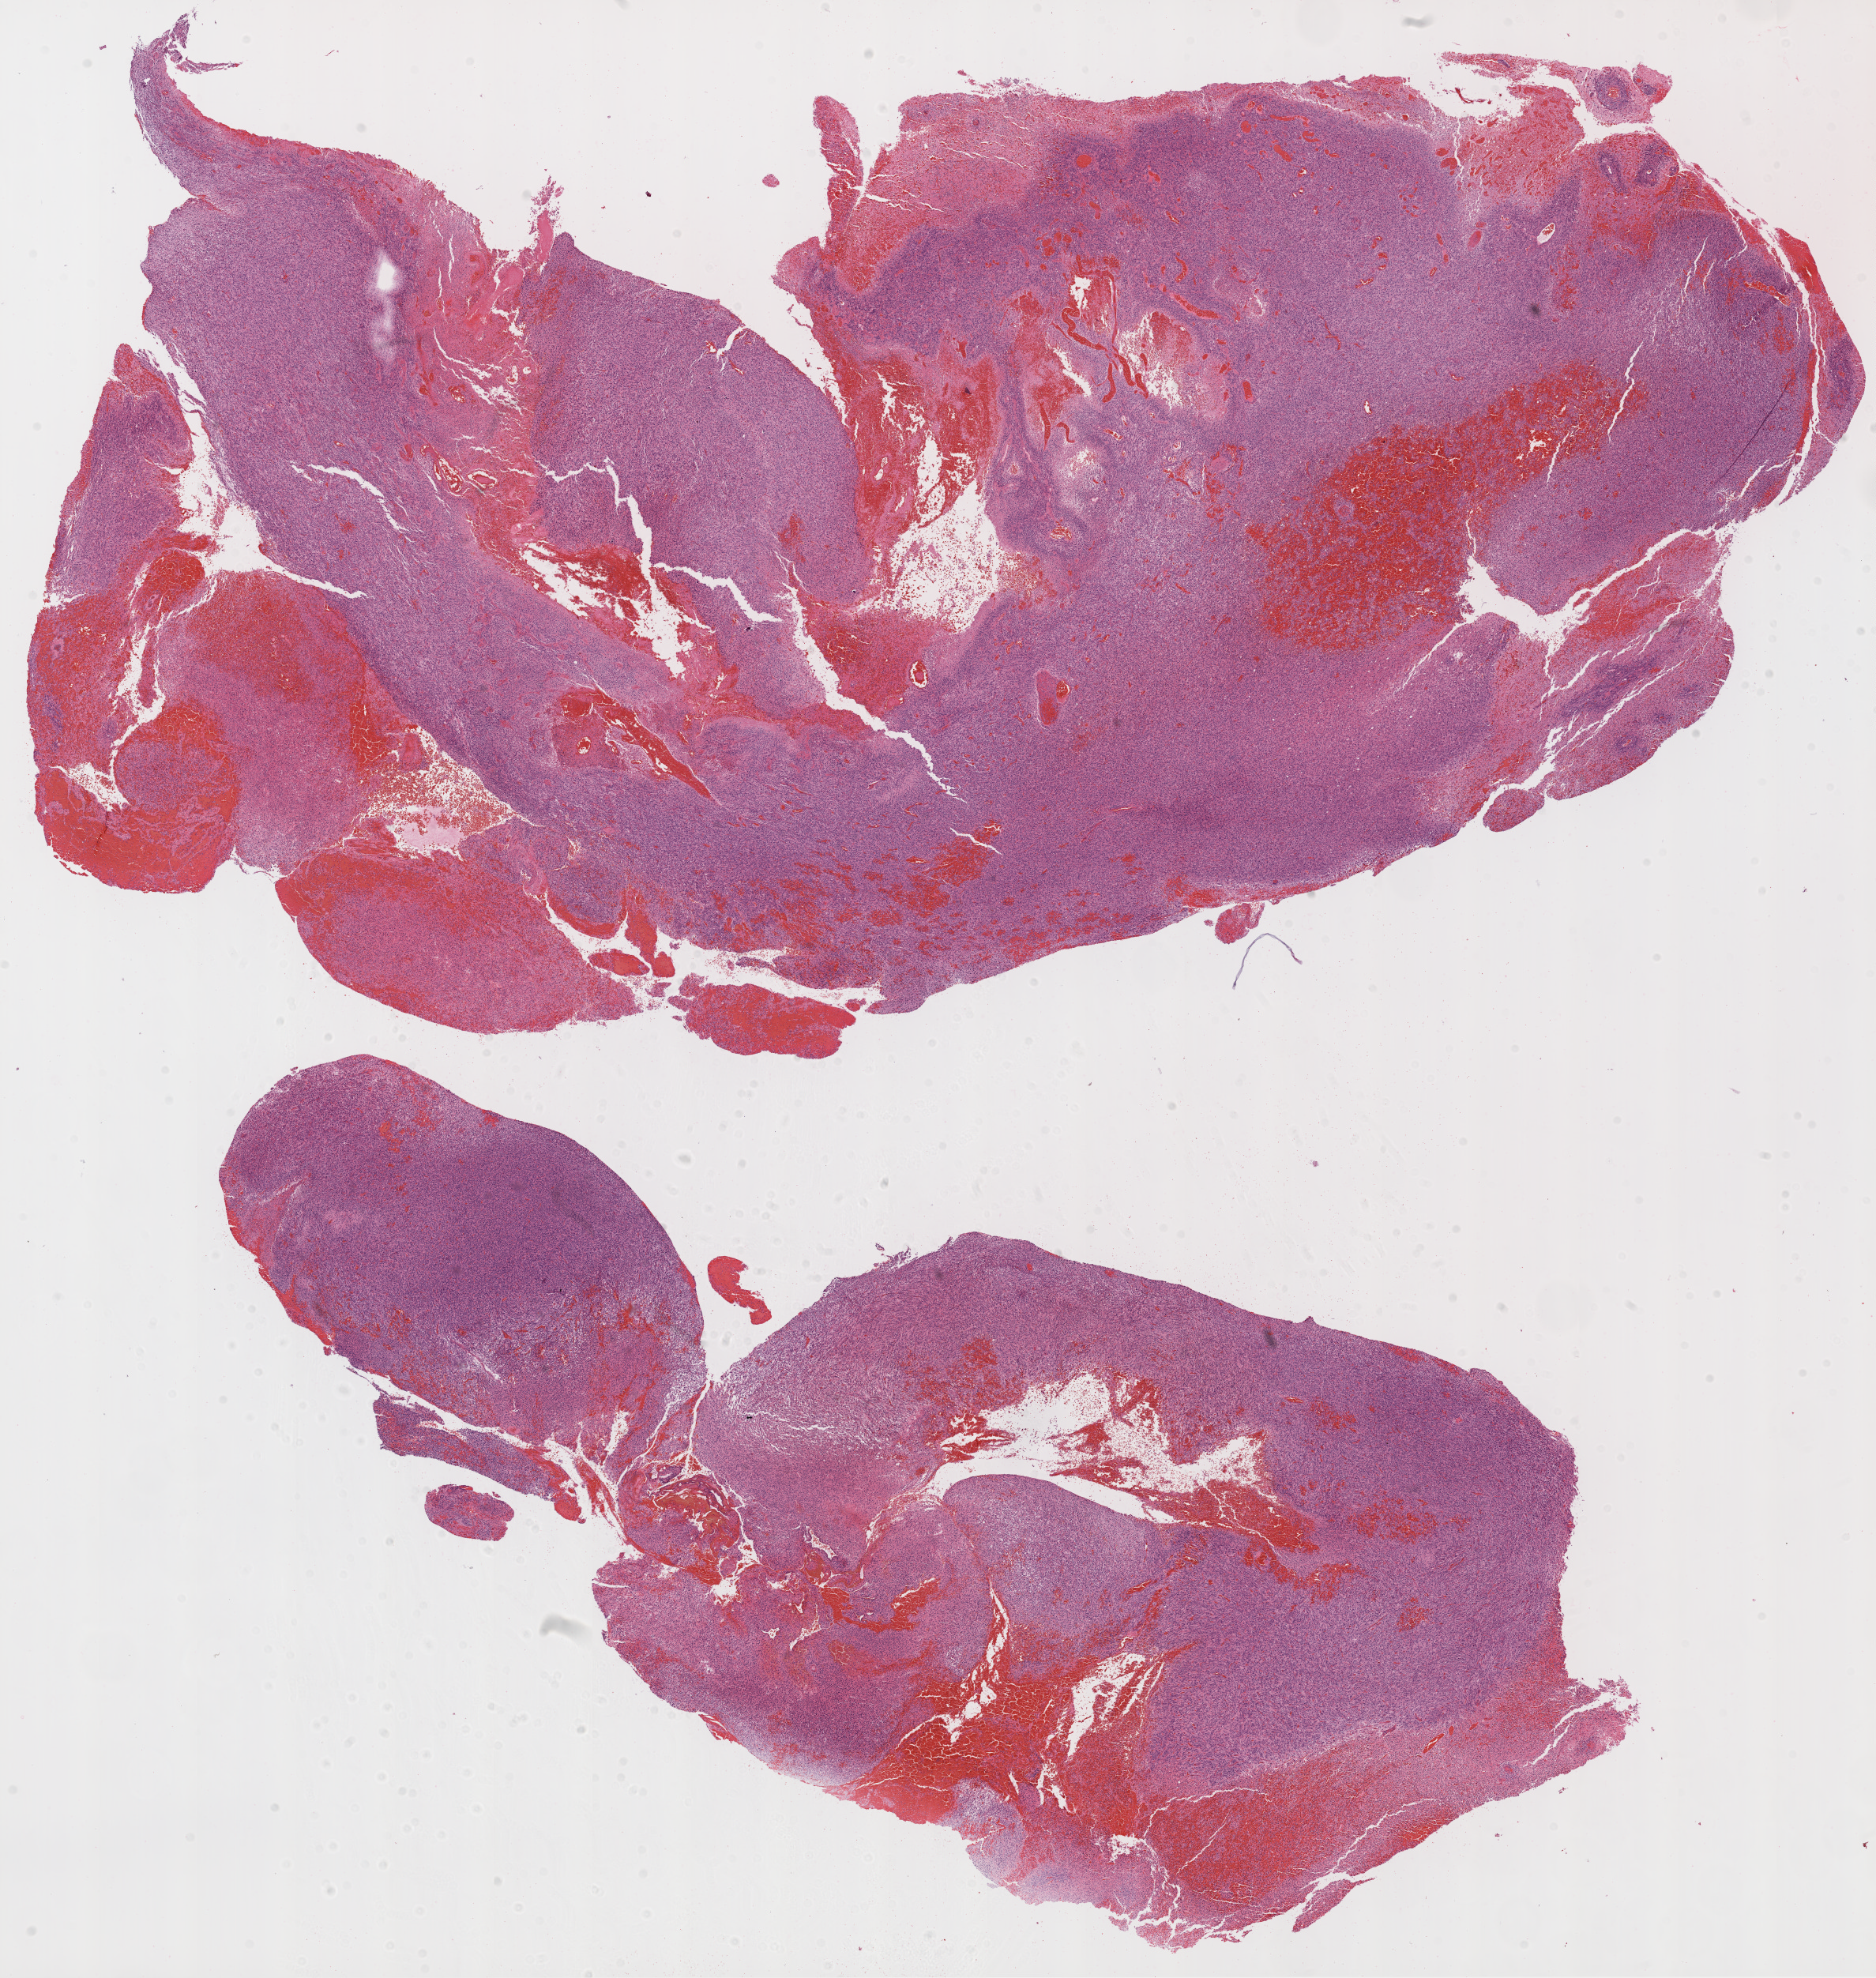
Hematoxylin and eosin (H&E) stained whole-slide image, low-resolution overview of the scanned area, about 19.1 x 20.1 mm (slide scanned at 20x); formalin-fixed paraffin-embedded (FFPE) diagnostic section; primary tumour sample from the brain. Female, age 53 years at initial diagnosis.
Histologic diagnosis: Glioblastoma.